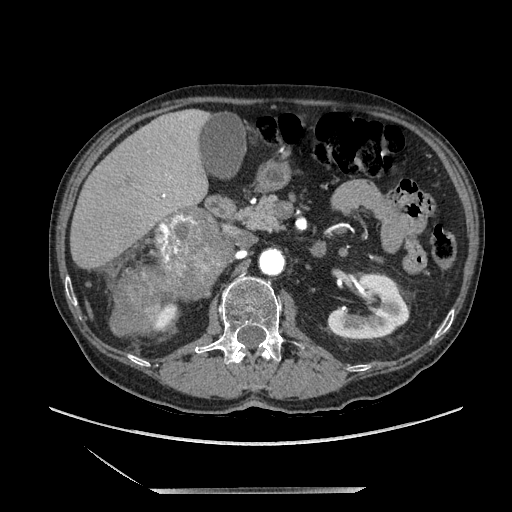
Contrast-enhanced abdominal CT, one axial slice. Position 102 of 243 along the scan axis. Soft-tissue window (W 400 / L 40 HU). 512 × 512 image matrix, field of view 420 × 420 mm. Male patient. Case-level facts recorded for this patient, not image findings: diagnosis: adrenocortical carcinoma; tumour side: right adrenal; tumour size at pathology: 16 cm; Ki-67 index: 17 %; stage (as recorded): 3.
Annotated regions visible in this slice (semi-automatically segmented with operator editing):
- mass: box from (x=113, y=209) to (x=226, y=336) px